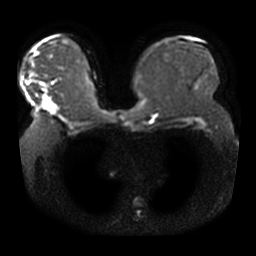
Breast MRI, one axial slice; position 24 of 42 along the scan axis; diffusion-weighted series; image 2 of 4 stored at this slice position (different b-values; order by instance number); 3 T; 256 × 256 image matrix. Female patient.
Structures marked on this image (manually delineated by an expert):
- tumour on diffusion-weighted imaging: box from (x=44, y=98) to (x=57, y=114) px